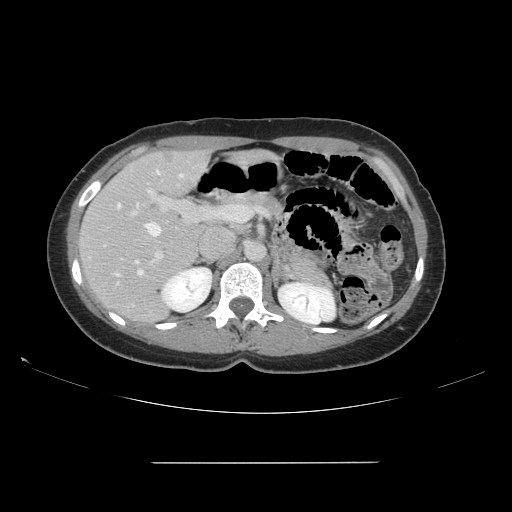
Contrast-enhanced abdominal CT, one axial slice; slice 93 of 151 in the series (ordered by position); 120 kVp; intravenous contrast given; soft-tissue window (W 400 / L 40 HU); 2.5 mm slice thickness; 512 × 512 image matrix, field of view 421 × 421 mm. Female patient, age 46 years. From the clinical record (not read from this slice): diagnosis: colorectal cancer liver metastases, imaged before liver resection; multiple liver metastases: yes; largest metastasis: 3 cm; chemotherapy before resection: no.
Outlined on this slice (outlined manually by an expert reader):
- hepatic veins: box from (x=116, y=171) to (x=184, y=277) px
- liver: (x=81, y=150)–(x=209, y=323)
- planned liver remnant (the part of the liver to remain after resection): (x=91, y=152)–(x=207, y=269)
- portal vein (with intrahepatic branches): (x=129, y=182)–(x=247, y=266)
- liver metastasis: (x=164, y=156)–(x=173, y=162)